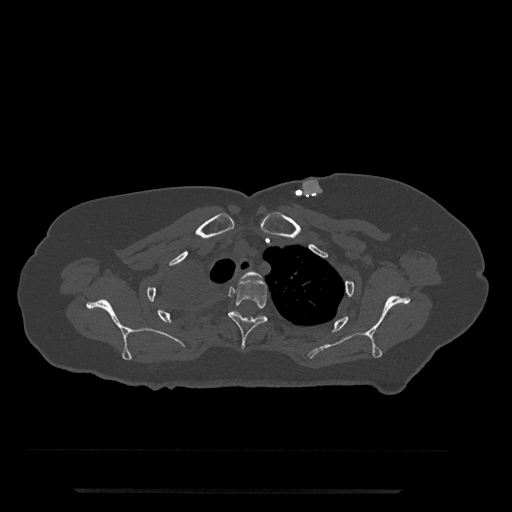
CT including the spine, one axial slice. Slice 630 of 797 in the series (ordered by position). 120 kVp. Bone window (W 1800 / L 400 HU). 0.5 mm slice thickness. 512 × 512 image matrix. Patient: female, 51 years. From the clinical record (not read from this slice): primary cancer: neuro; vertebrae with lytic lesions (as recorded): T8.
Structures marked on this image (semi-automatically segmented with operator editing):
- T2 vertebra: bounding box <241,270,260,279> (left, top, right, bottom; pixels)
- T3 vertebra: <228,275,268,350>
- T4 vertebra: <233,311,264,318>